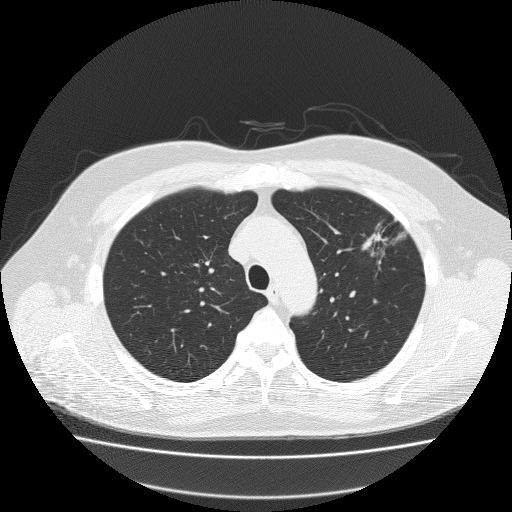
Low-dose screening chest CT, one axial slice. Slice 154 of 204 in the series (ordered by position). 120 kVp. Lung window (W 1500 / L -600 HU). 2 mm slice thickness. 512 × 512 image matrix, field of view 410 × 410 mm.
Outlined on this slice (manually delineated by an expert):
- lesion 1 (tumor, upper lobe of left lung): box from (x=362, y=222) to (x=392, y=256) px